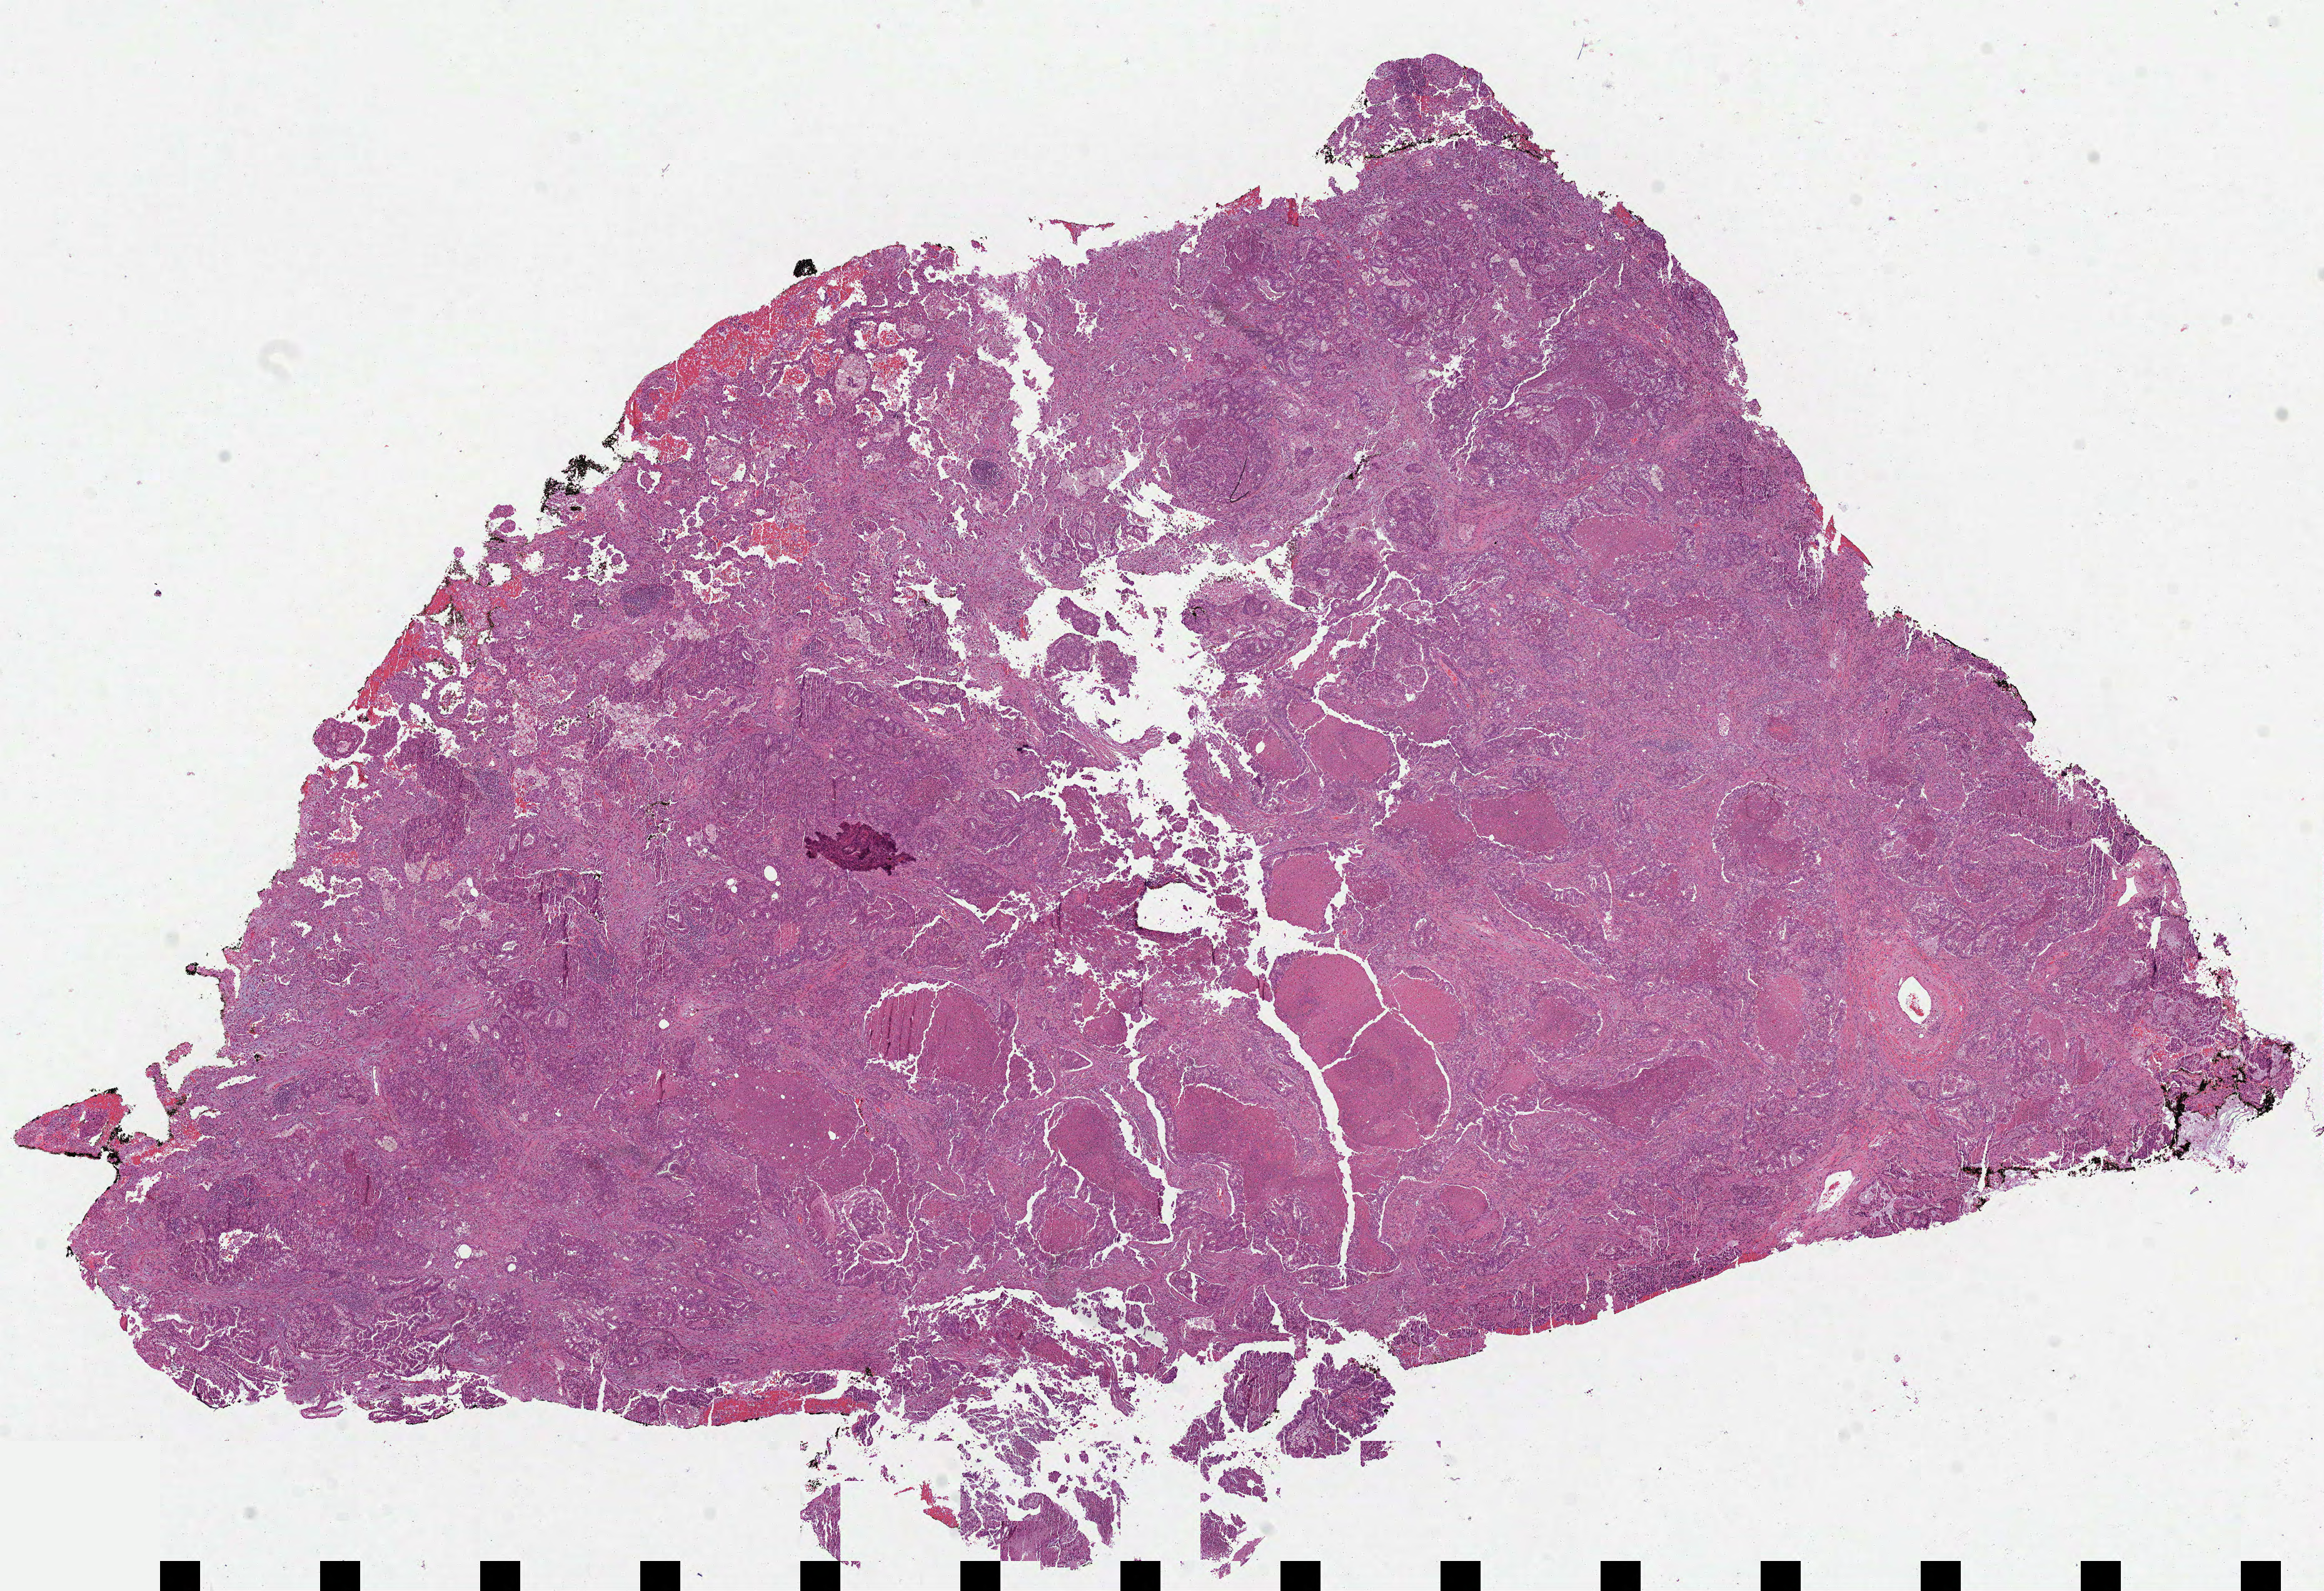
Whole-slide histology image, H&E, shown as a low-resolution overview of the whole scanned area (about 15.0 x 10.3 mm), formalin-fixed paraffin-embedded (FFPE) diagnostic section, lung, primary tumour sample. Male, age 67 years at initial diagnosis.
TNM: T3 N2 MX. Diagnosis: Adenocarcinoma, NOS (middle lobe, lung). Laterality: right. AJCC pathologic stage: IIIA.